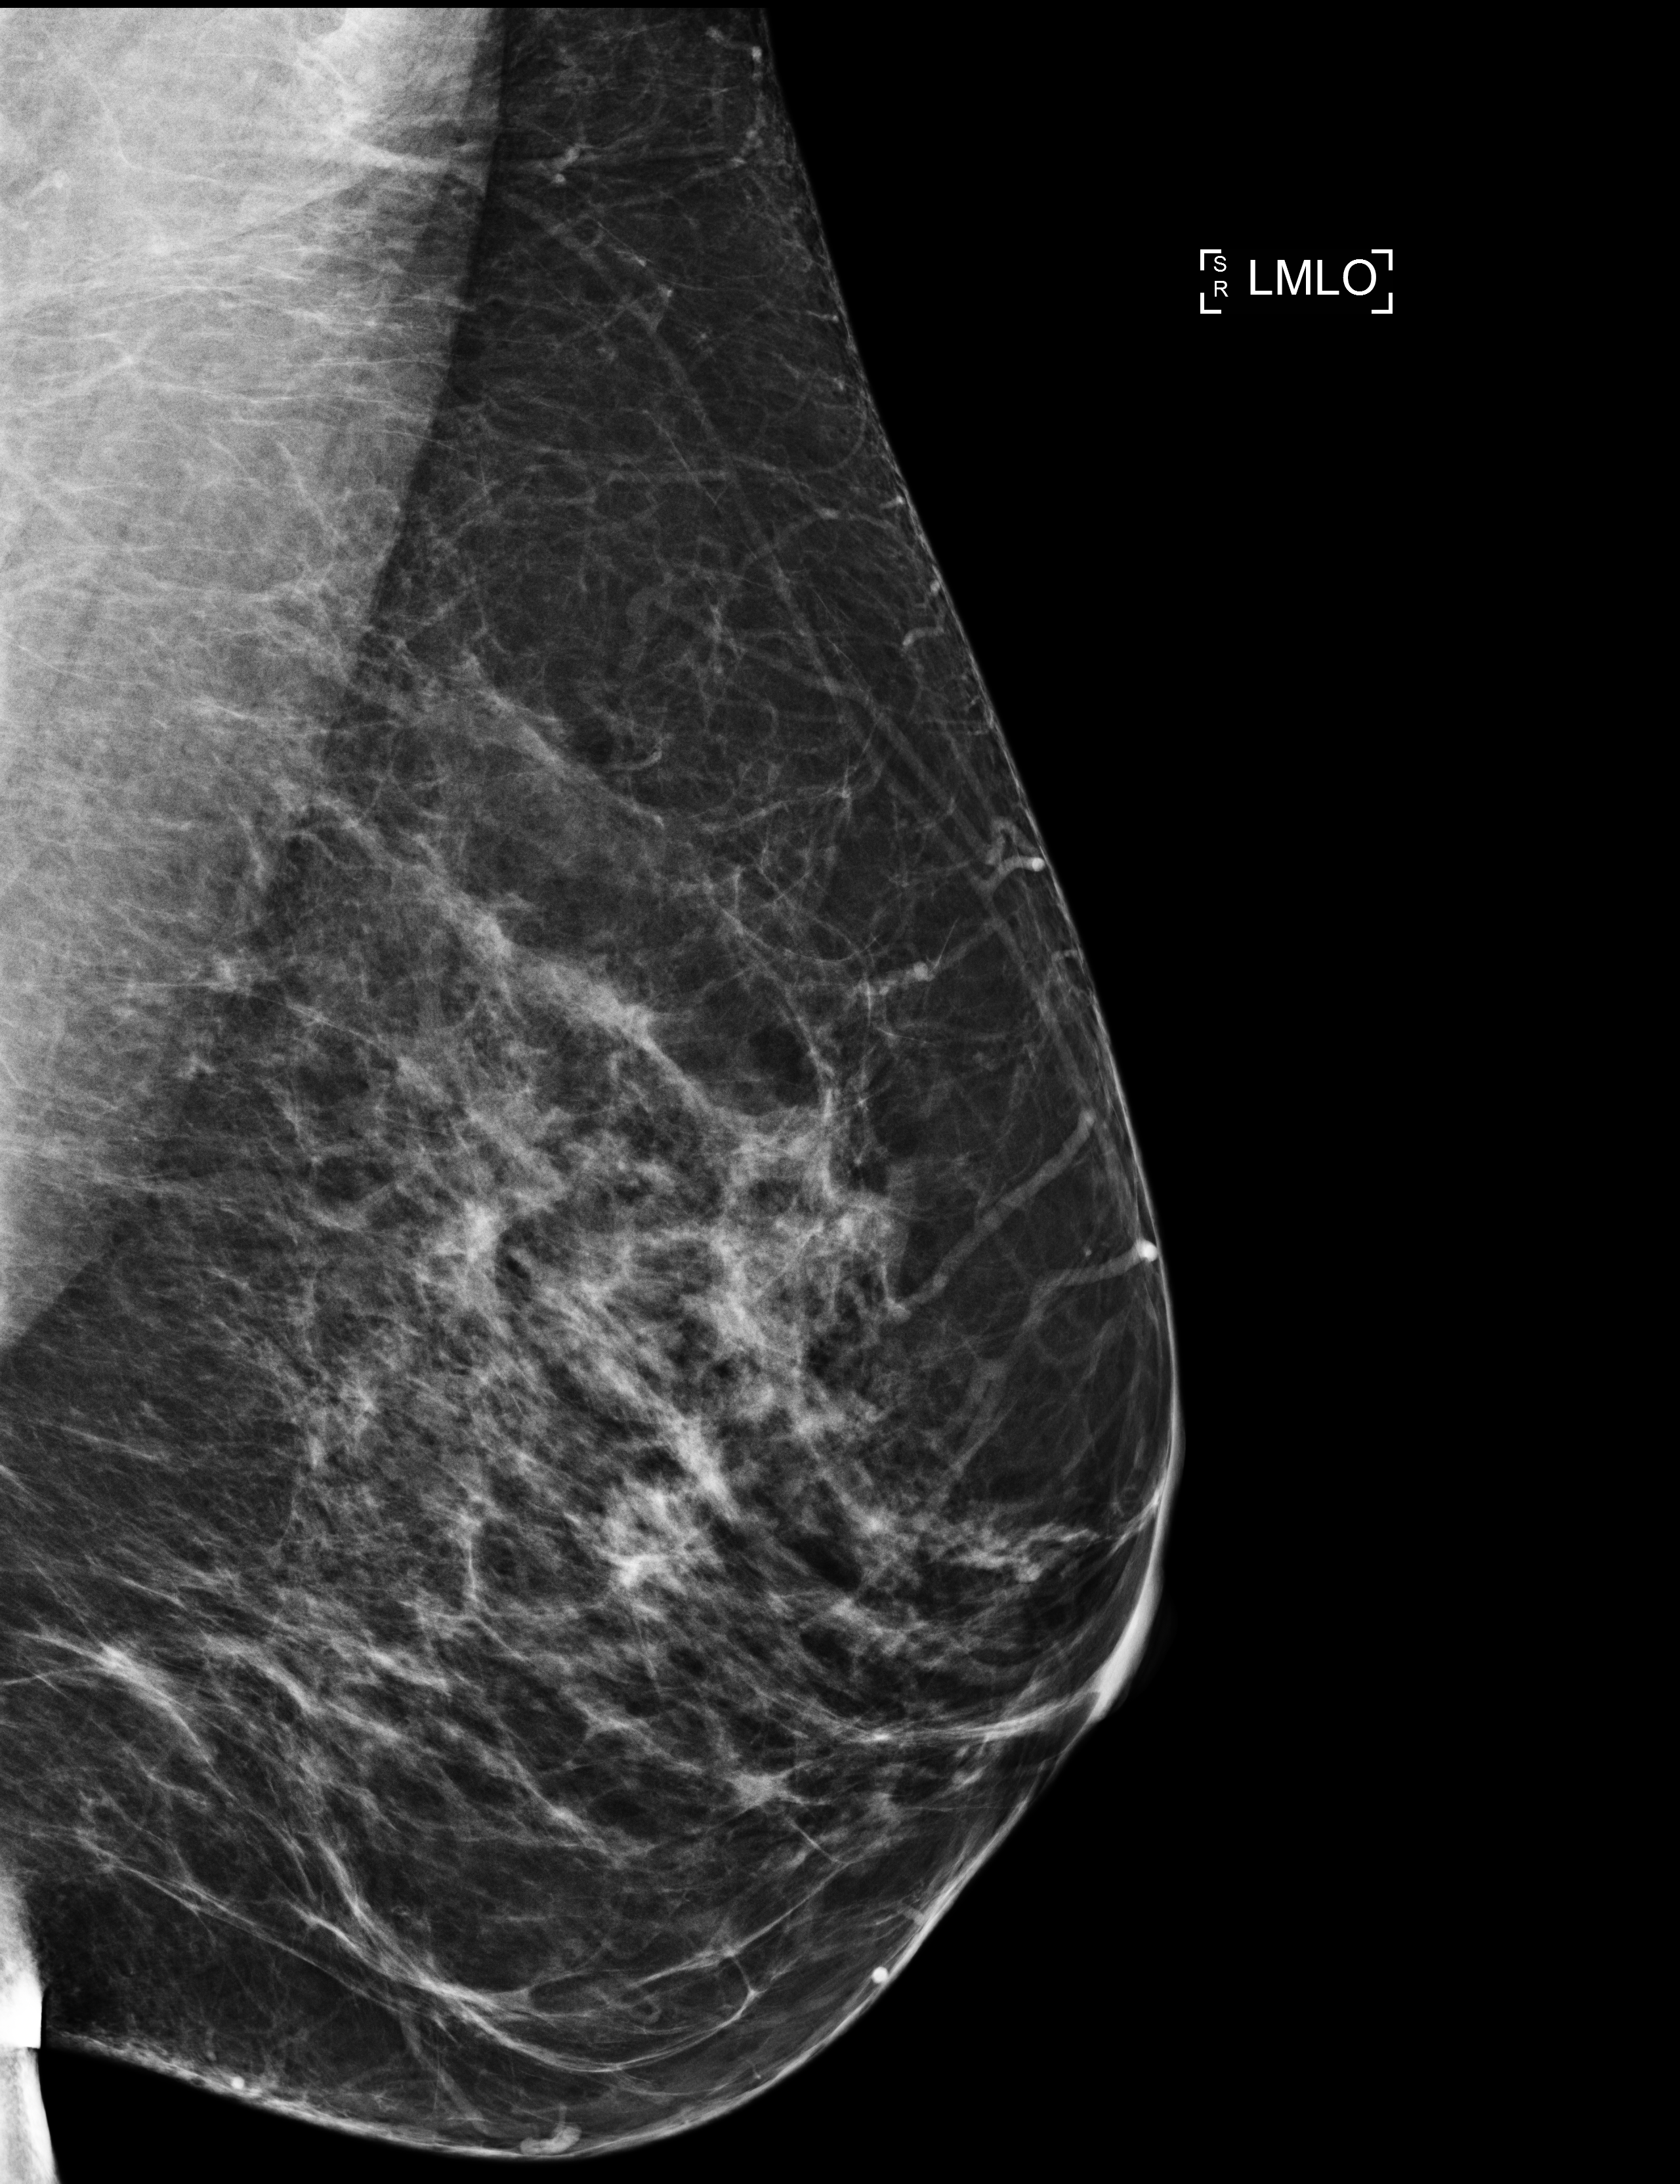
Annual screening mammography examination. Patient aged 50 years (female).
Image type: full-field digital mammogram. Breast: left. Projection: mediolateral oblique (MLO) view. BI-RADS breast density category at the screening exam (both breasts, scale 1–4): 3. Final BI-RADS assessment for this screening round (tomosynthesis exam, both breasts): category 1. Recall: no recall after this screen.